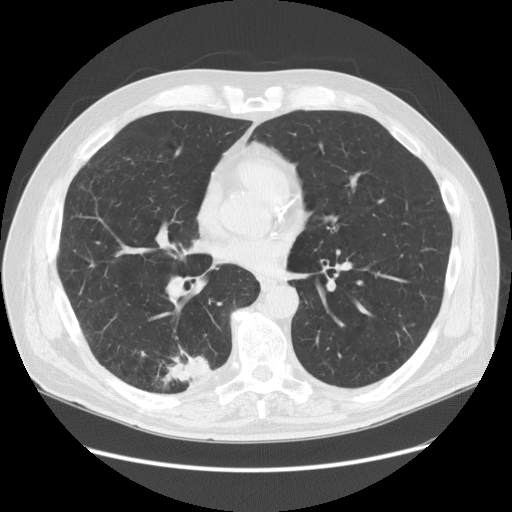
Low-dose screening chest CT, axial slice. First (baseline) screen. Lung window (W 1500 / L -600 HU). Standard (soft-tissue) reconstruction kernel (STANDARD). Slice 80 of 149 in the series. 512 × 512 image matrix. Male participant, aged 68 years at enrolment.
- Lesion marked by an expert reader, bounding box <125,336,226,409> (left, top, right, bottom; pixels).
- Screening reader's record for this exam (one nodule recorded; not confirmed to be the boxed lesion): non-calcified nodule or mass ≥4 mm, right lower lobe, 37 × 20 mm, spiculated (stellate) margins, soft tissue attenuation.
- Official screen result: positive, change unspecified: nodule(s) >= 4 mm or enlarging nodule(s), mass(es), or other non-specific abnormalities suspicious for lung cancer.
- Later outcome: lung cancer diagnosed 24 days after this screen — adenosquamous carcinoma, right lower lobe, poorly differentiated (G3), stage IIIA (AJCC 6th edition), 30 mm at pathology.